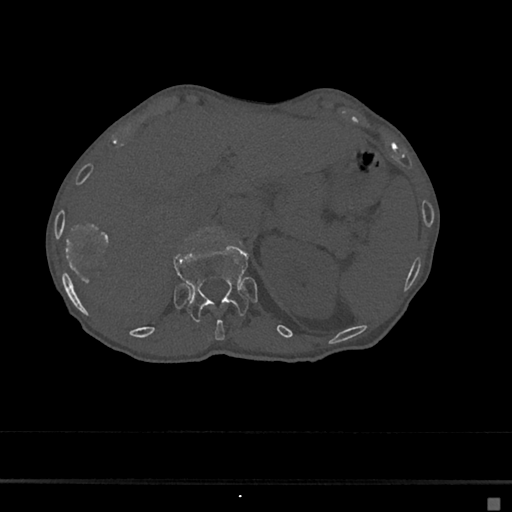
CT including the spine, one axial slice; position 130 of 797 along the scan axis; bone window (W 1800 / L 400 HU); 512 × 512 image matrix, field of view 360 × 360 mm. Female patient, age 68 years. Case-level facts recorded for this patient, not image findings: primary cancer: renal.
Outlined on this slice (semi-automatic segmentation, software-assisted and operator-edited):
- T11 vertebra: box from (x=215, y=319) to (x=225, y=341) px
- T12 vertebra: (x=173, y=244)–(x=248, y=322)